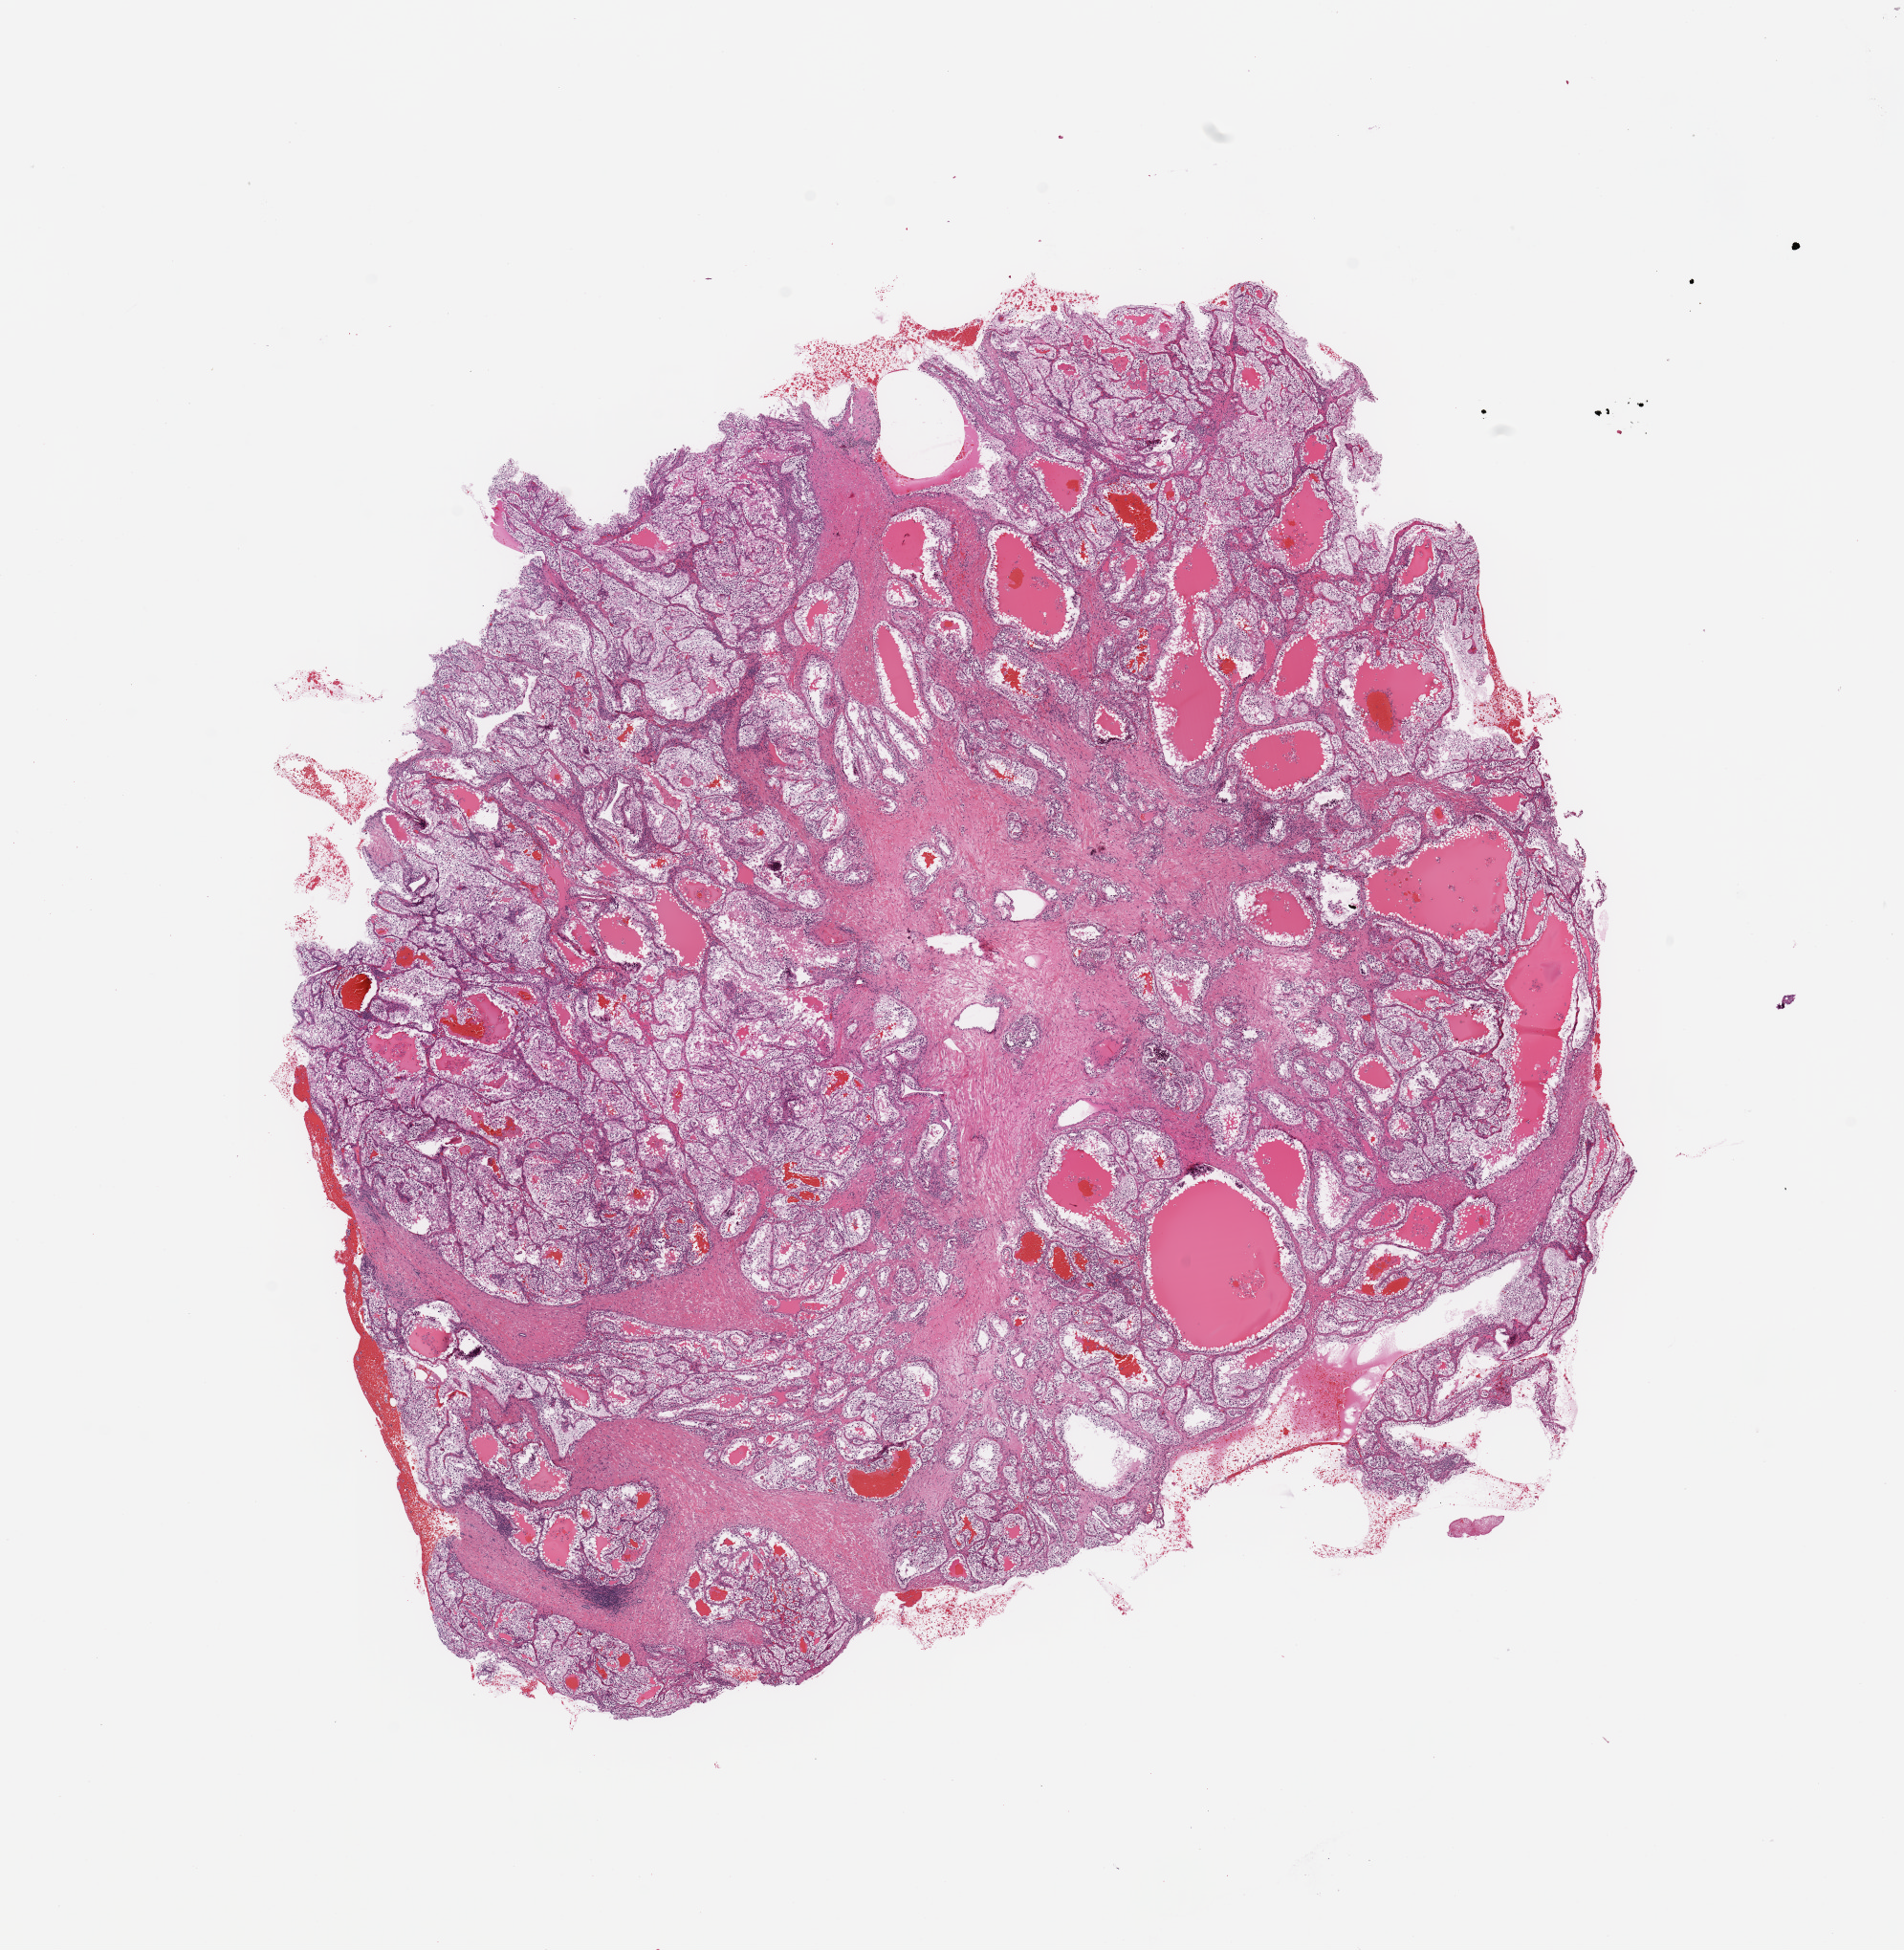
H&E-stained whole-slide image — a low-resolution overview of the entire scanned area, about 15.8 x 16.1 mm (acquisition: 20x scan); tumour tissue sample, sampled site: kidney. Patient: male, age 55 years. Composition of this section per pathologist review: tumour nuclei 85%, necrosis 2%.
Histologic diagnosis: Renal cell carcinoma, NOS.